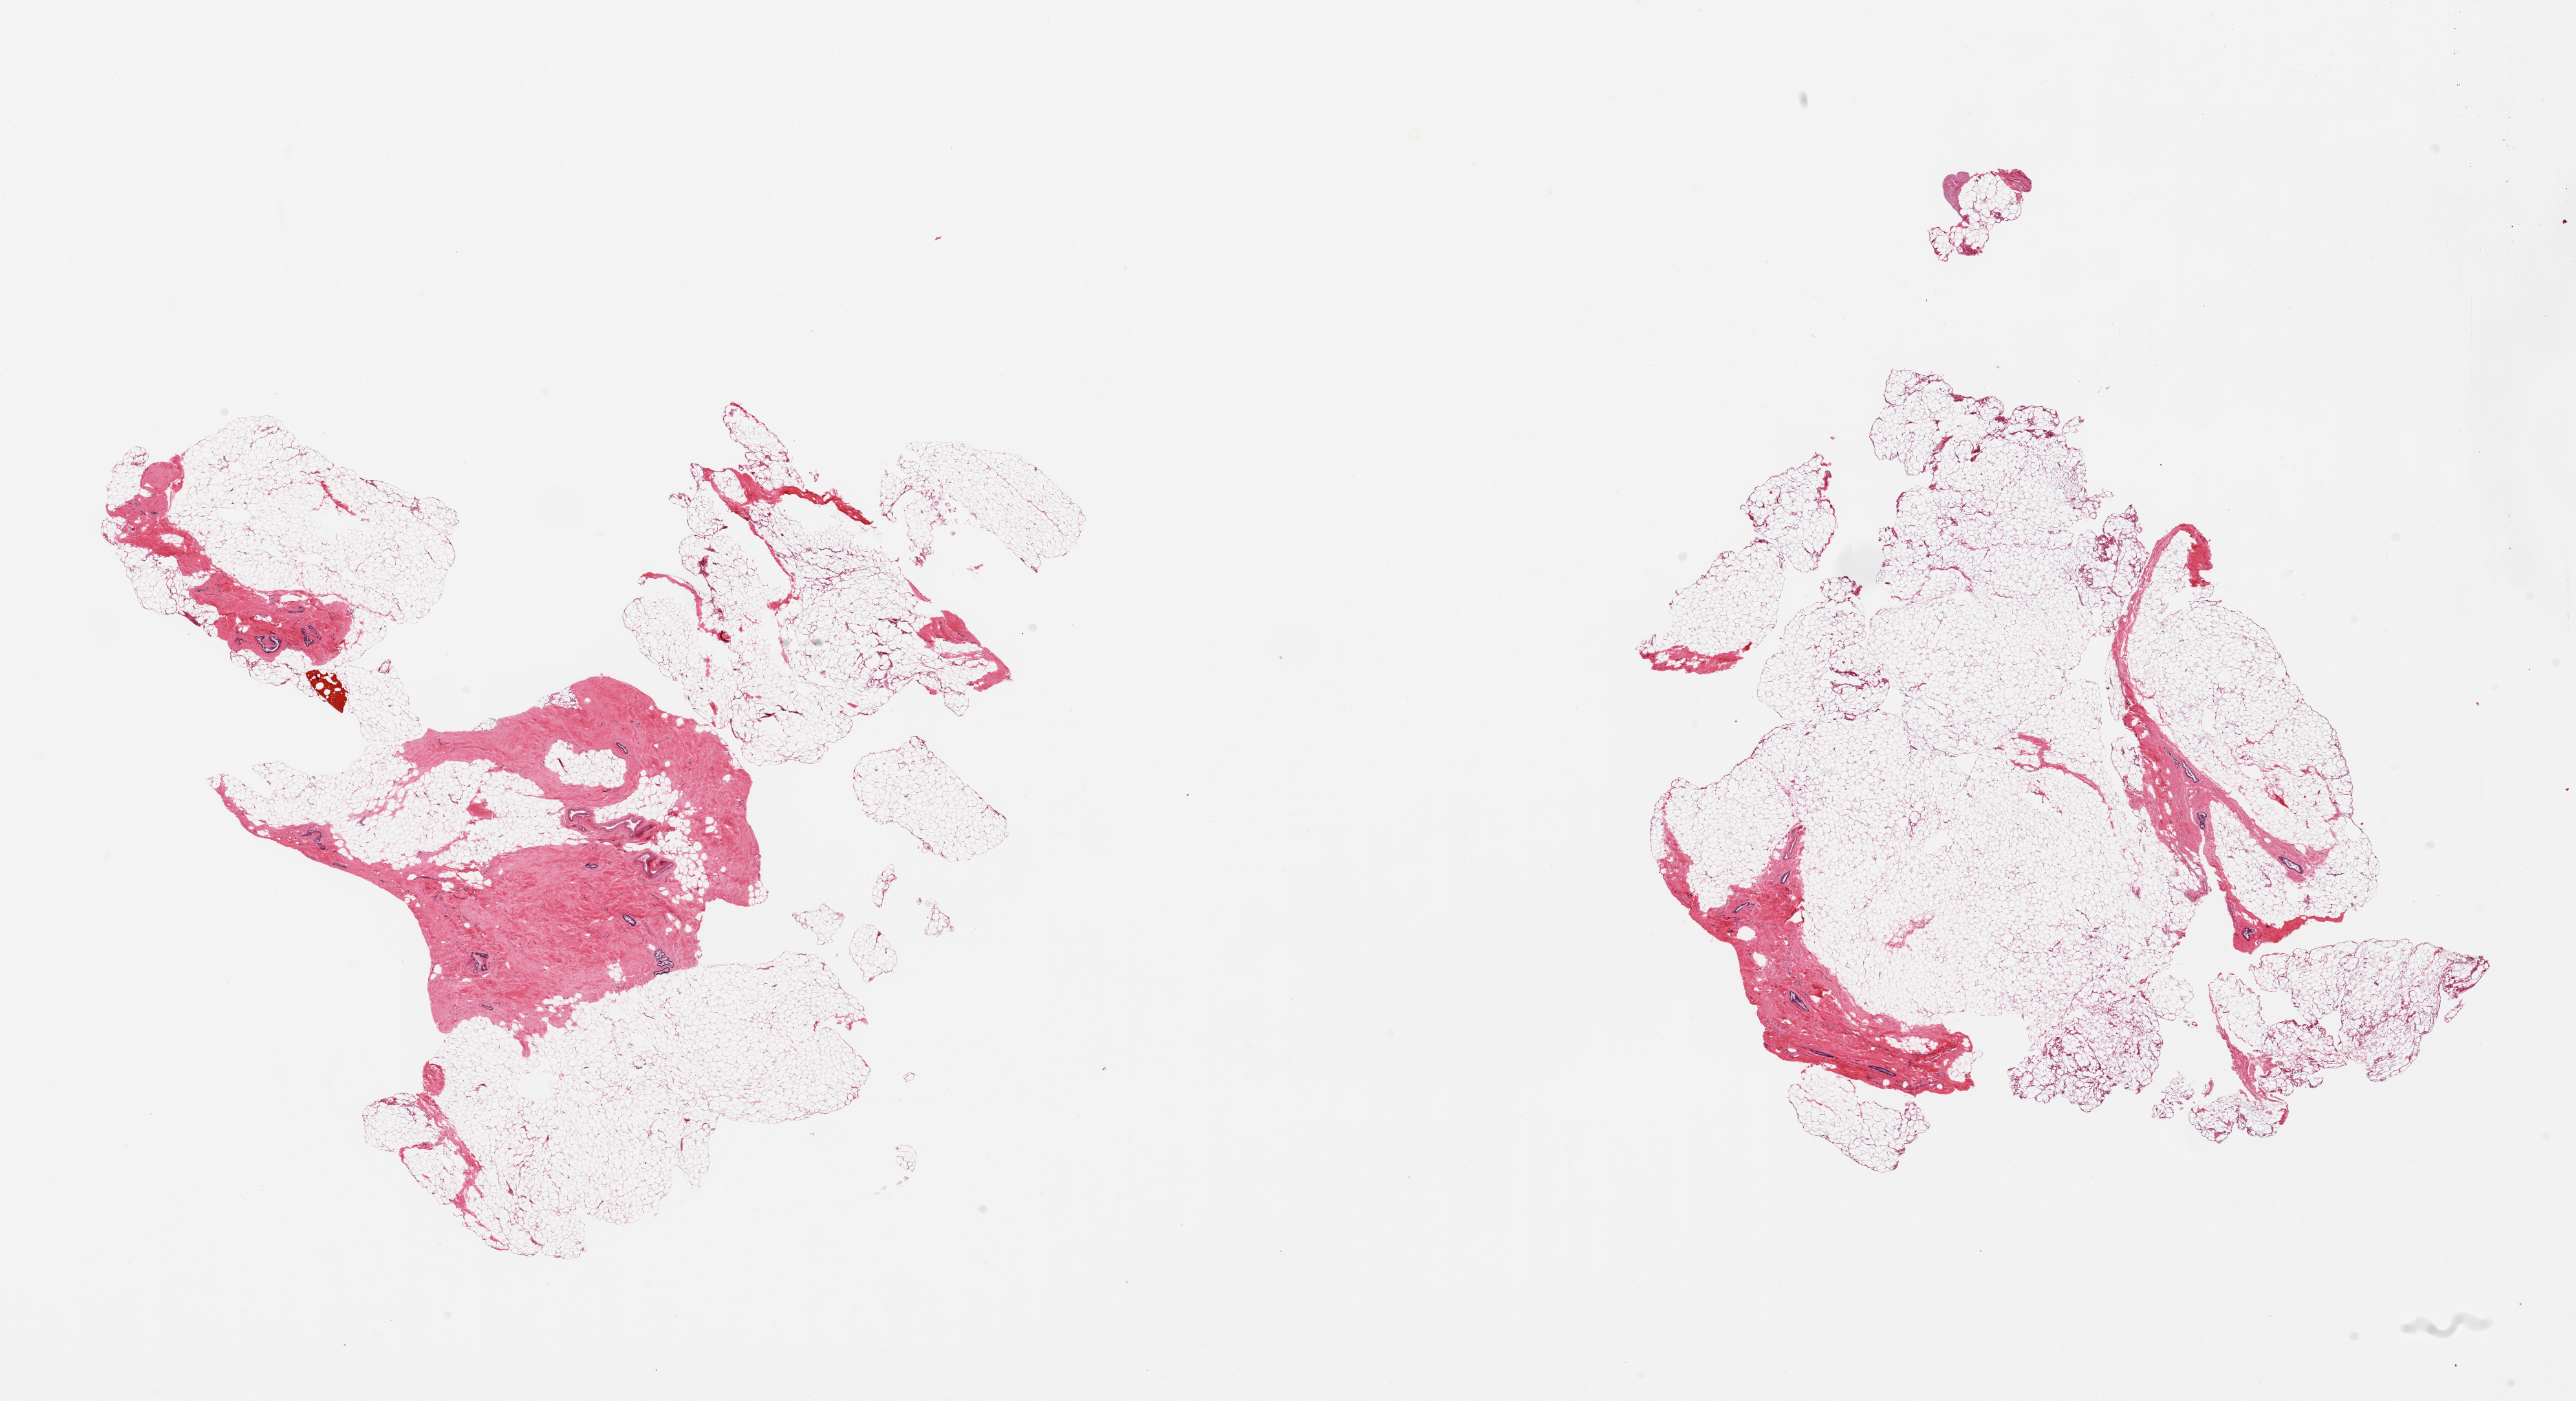
Digitized haematoxylin and eosin-stained section — low-resolution overview of the scanned area, about 31.5 x 17.1 mm (from a 20x scan), PAXgene-fixed paraffin-embedded (PFPE) section, section of breast (target tissue), donor tissue sample. Donor sex: male.
- reviewer comment on this tissue sample: 2 pieces; predominantly fat with 10-20% stroma with scattered ducts